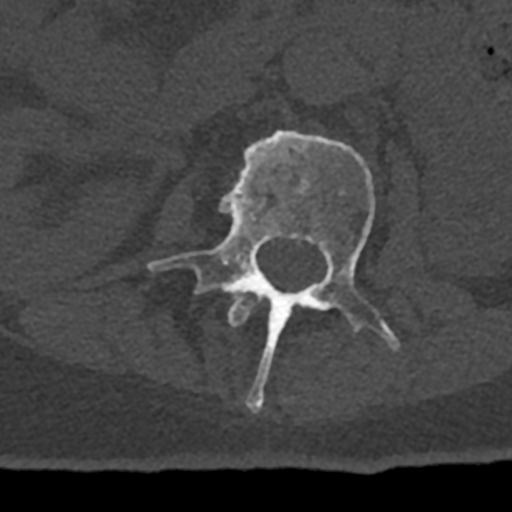
CT including the spine, one axial slice. Position 384 of 797 along the scan axis. 120 kVp. Bone window (W 1800 / L 400 HU). 0.5 mm slice thickness. 512 × 512 image matrix, field of view 160 × 160 mm. Male patient, age 74 years. From the clinical record (not read from this slice): primary cancer: renal; vertebrae with lytic lesions (as recorded): T10, L1, L2, L3, L4, L5.
Outlined on this slice (semi-automatic segmentation, software-assisted and operator-edited):
- L1 vertebra: bounding box <228,291,256,327> (left, top, right, bottom; pixels)
- L2 vertebra: <148,130,401,412>